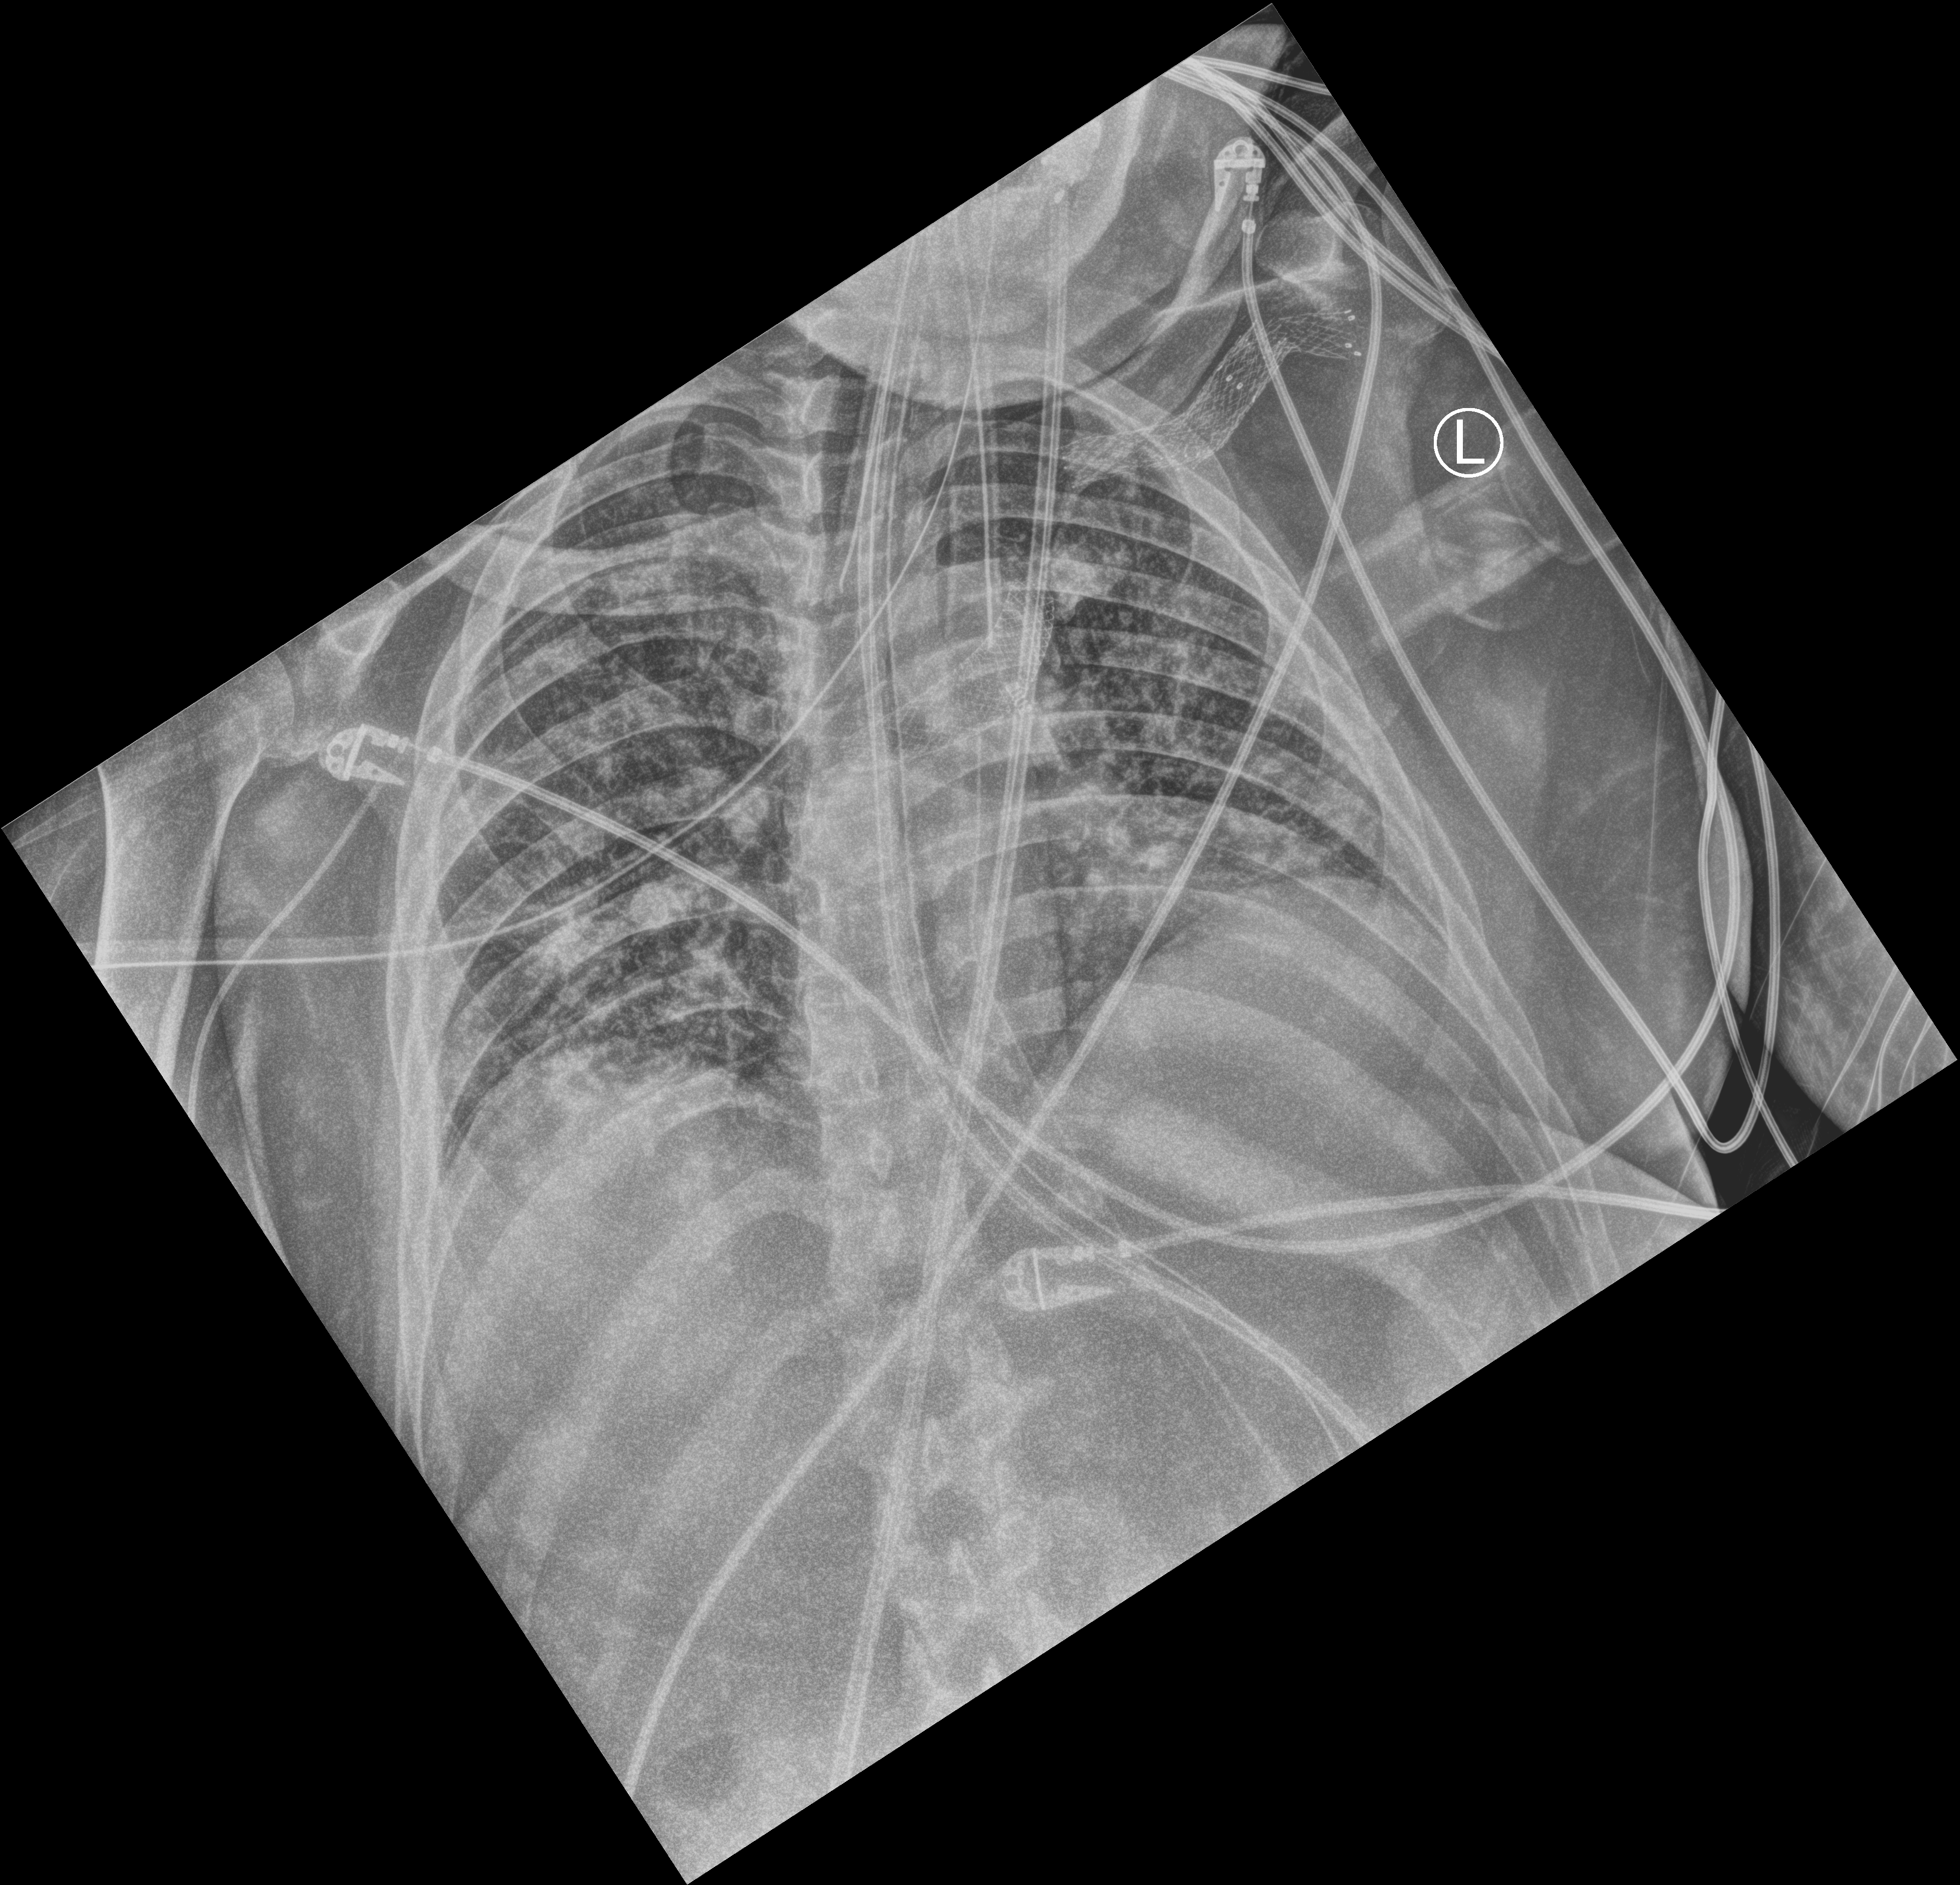
Portable chest radiograph; anteroposterior (AP) projection. Male patient hospitalised with COVID-19, age 18–59 years.
Admission-level facts for this patient (not findings on this image; timing relative to this image not recorded): length of hospital stay: 41 days.